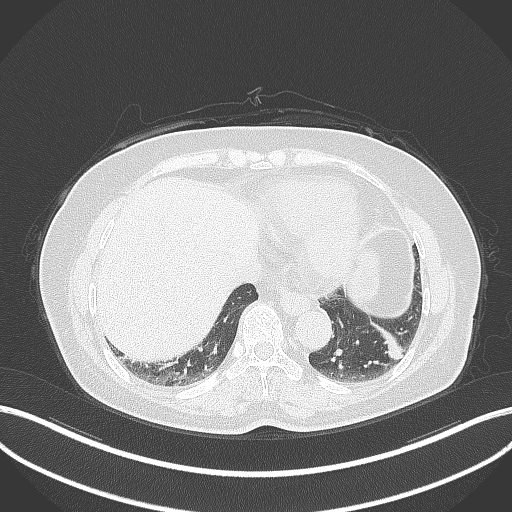
Chest CT, one axial slice. Slice 104 of 311 in the series (ordered by position). Reconstruction kernel B70f. 120 kVp. Lung window (W 1500 / L -600 HU). 512 × 512 image matrix. Patient: female, 59 years. Case-level facts recorded for this patient, not image findings: clinical TNM (as recorded): T2a N0 M0; histopathological grade: G2-3.
Annotated regions visible in this slice (bounding box drawn by a radiologist):
- lung tumour (recorded histology: adenocarcinoma): bounding box [x1, y1, x2, y2] px = [372, 320, 408, 364]